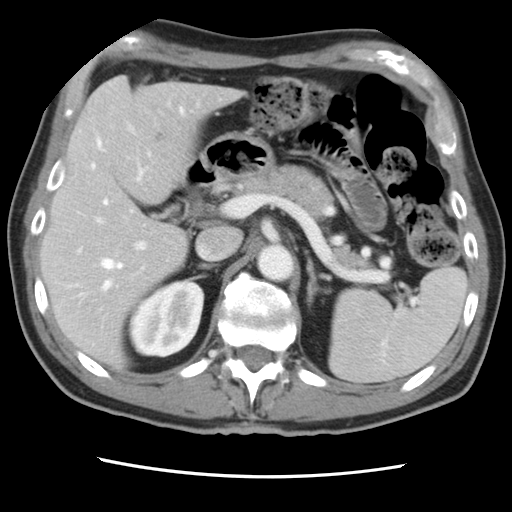
Contrast-enhanced abdominal CT, one axial slice. Position 50 of 83 along the scan axis. 120 kVp. Soft-tissue window (W 400 / L 40 HU). 512 × 512 image matrix, field of view 321 × 321 mm. Male patient, age 69 years. Case-level facts recorded for this patient, not image findings: diagnosis: colorectal cancer liver metastases, imaged before liver resection; multiple liver metastases: yes; largest metastasis: 3.5 cm; chemotherapy before resection: yes.
Structures marked on this image (expert manual segmentation):
- hepatic veins: bounding box <92,108,184,290> (left, top, right, bottom; pixels)
- liver: <43,78,237,366>
- planned liver remnant (the part of the liver to remain after resection): <43,137,188,366>
- portal vein (with intrahepatic branches): <77,153,230,254>